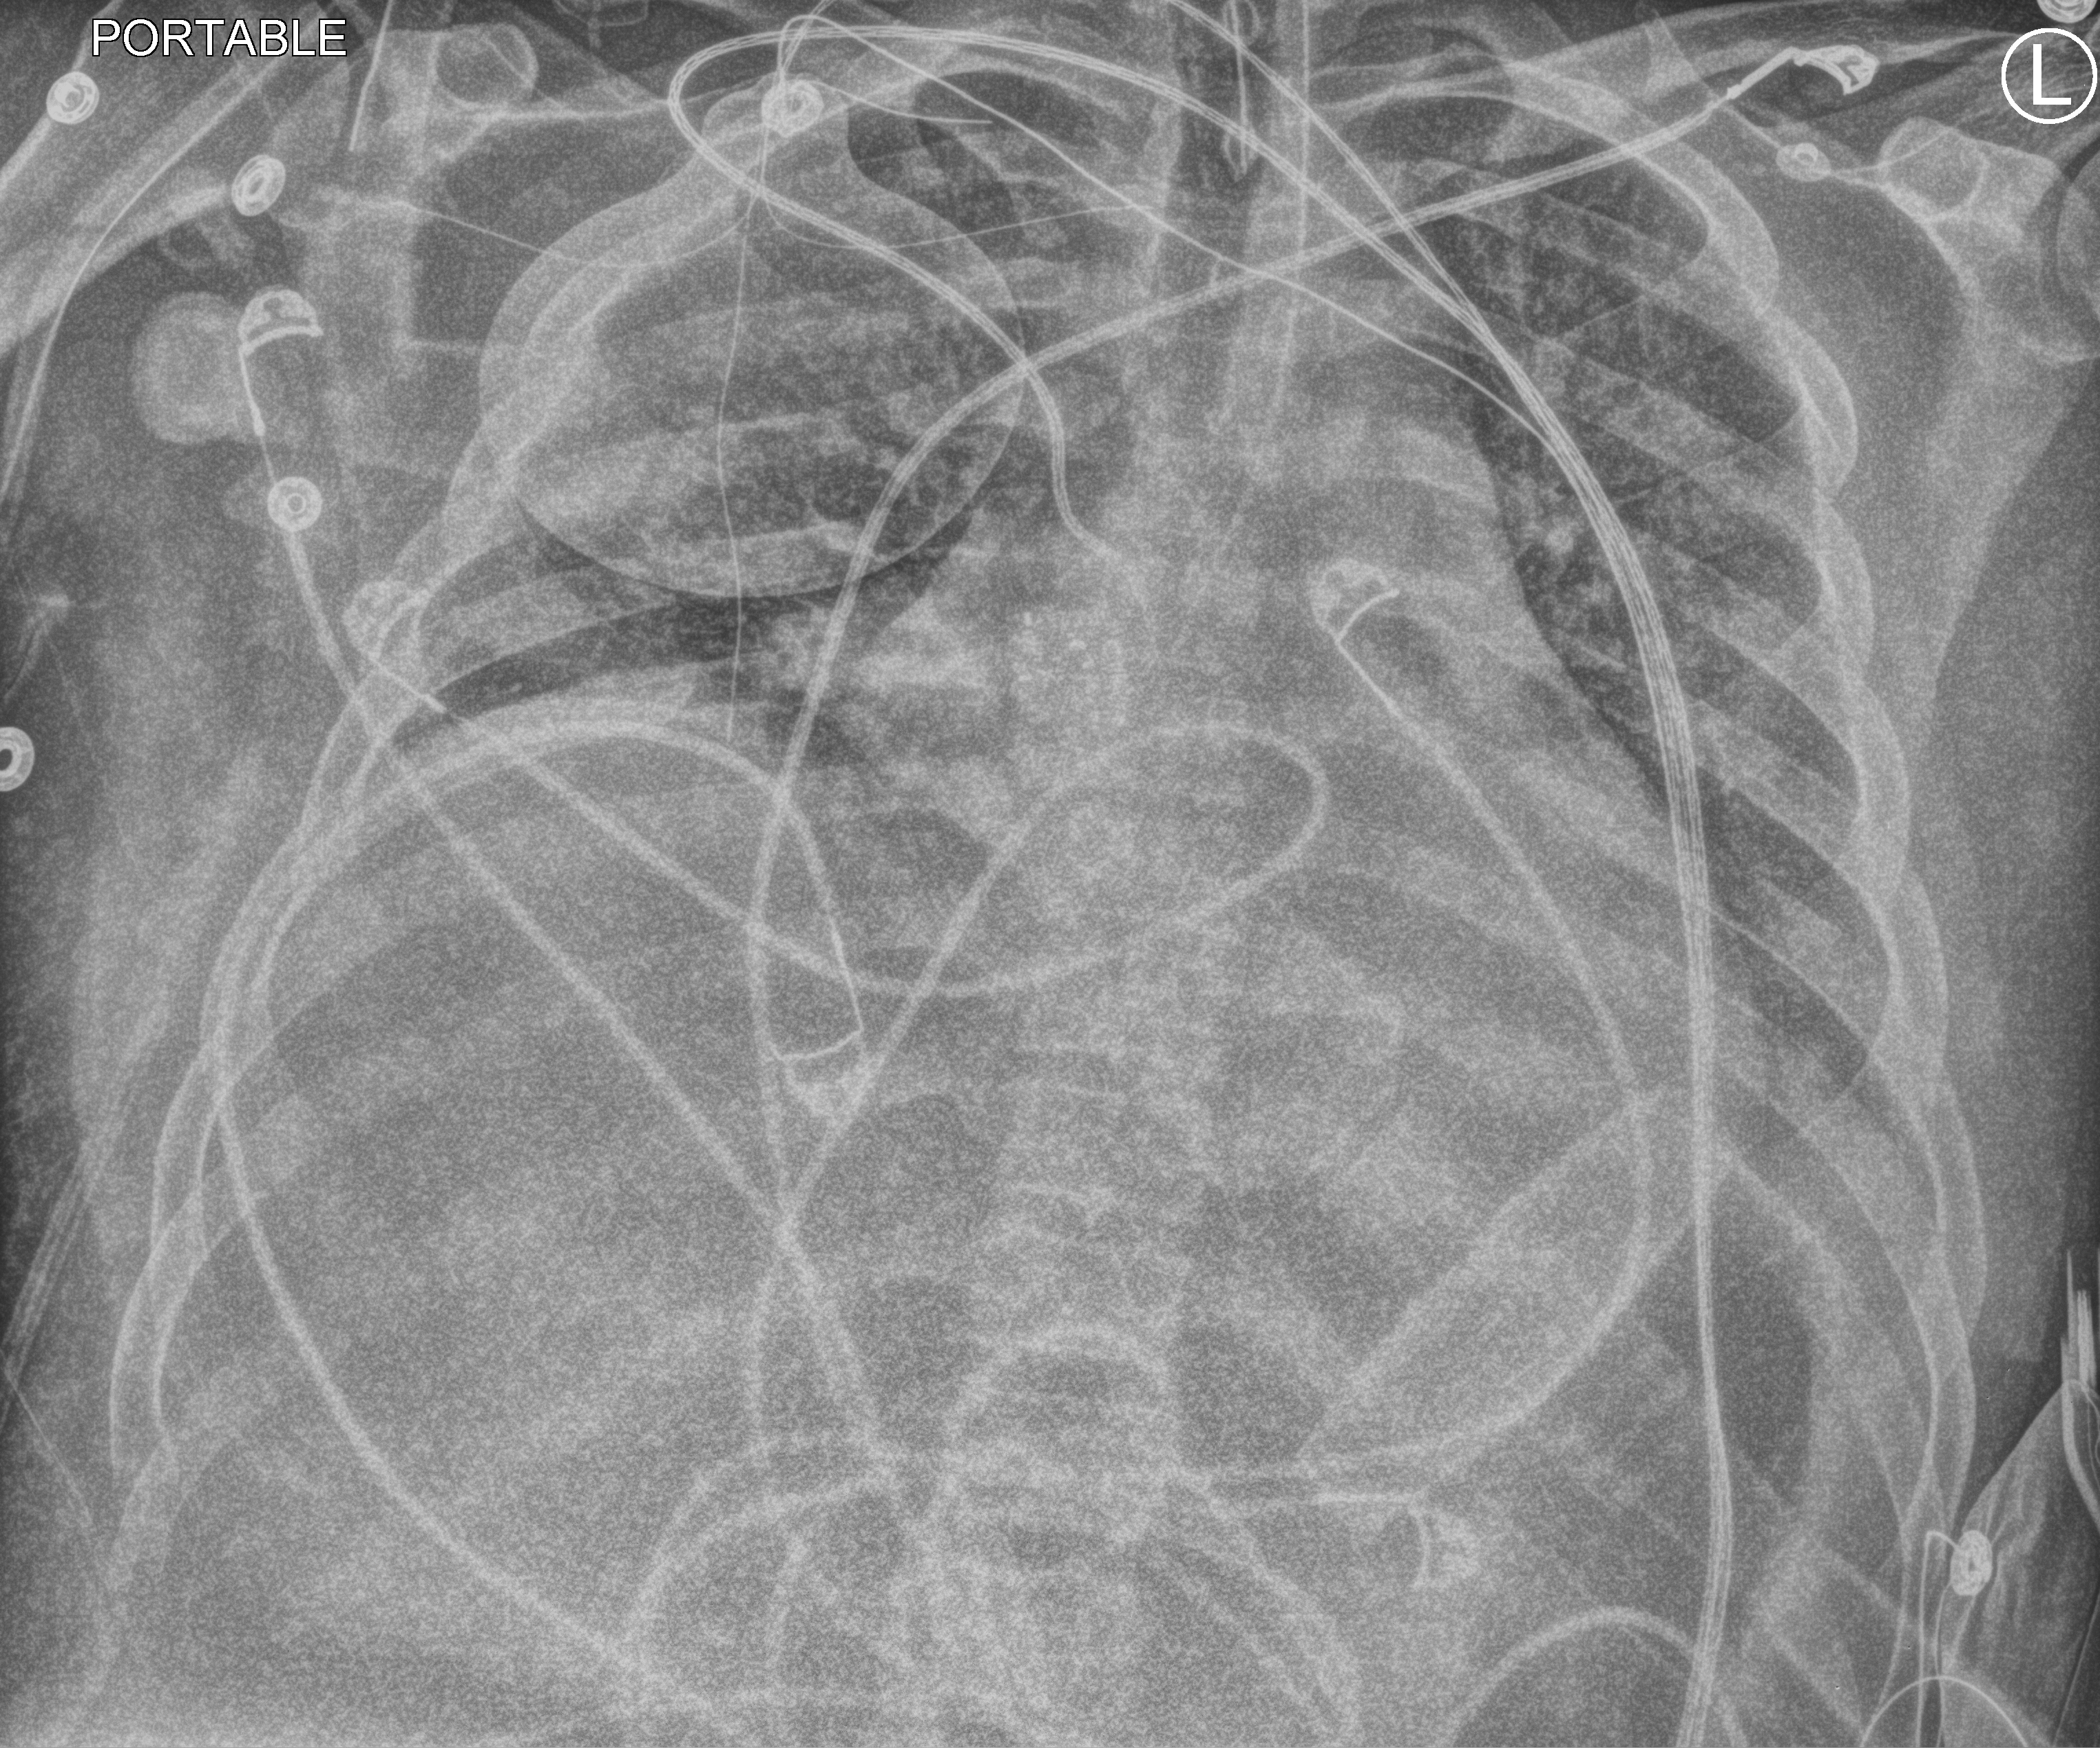
Portable chest radiograph; anteroposterior (AP) projection. Male patient hospitalised with COVID-19, age 18–59 years.
Hospital-stay facts (about this admission, not read from this image; timing relative to this image not recorded): length of hospital stay: 61 days; COPD (admission record): no.